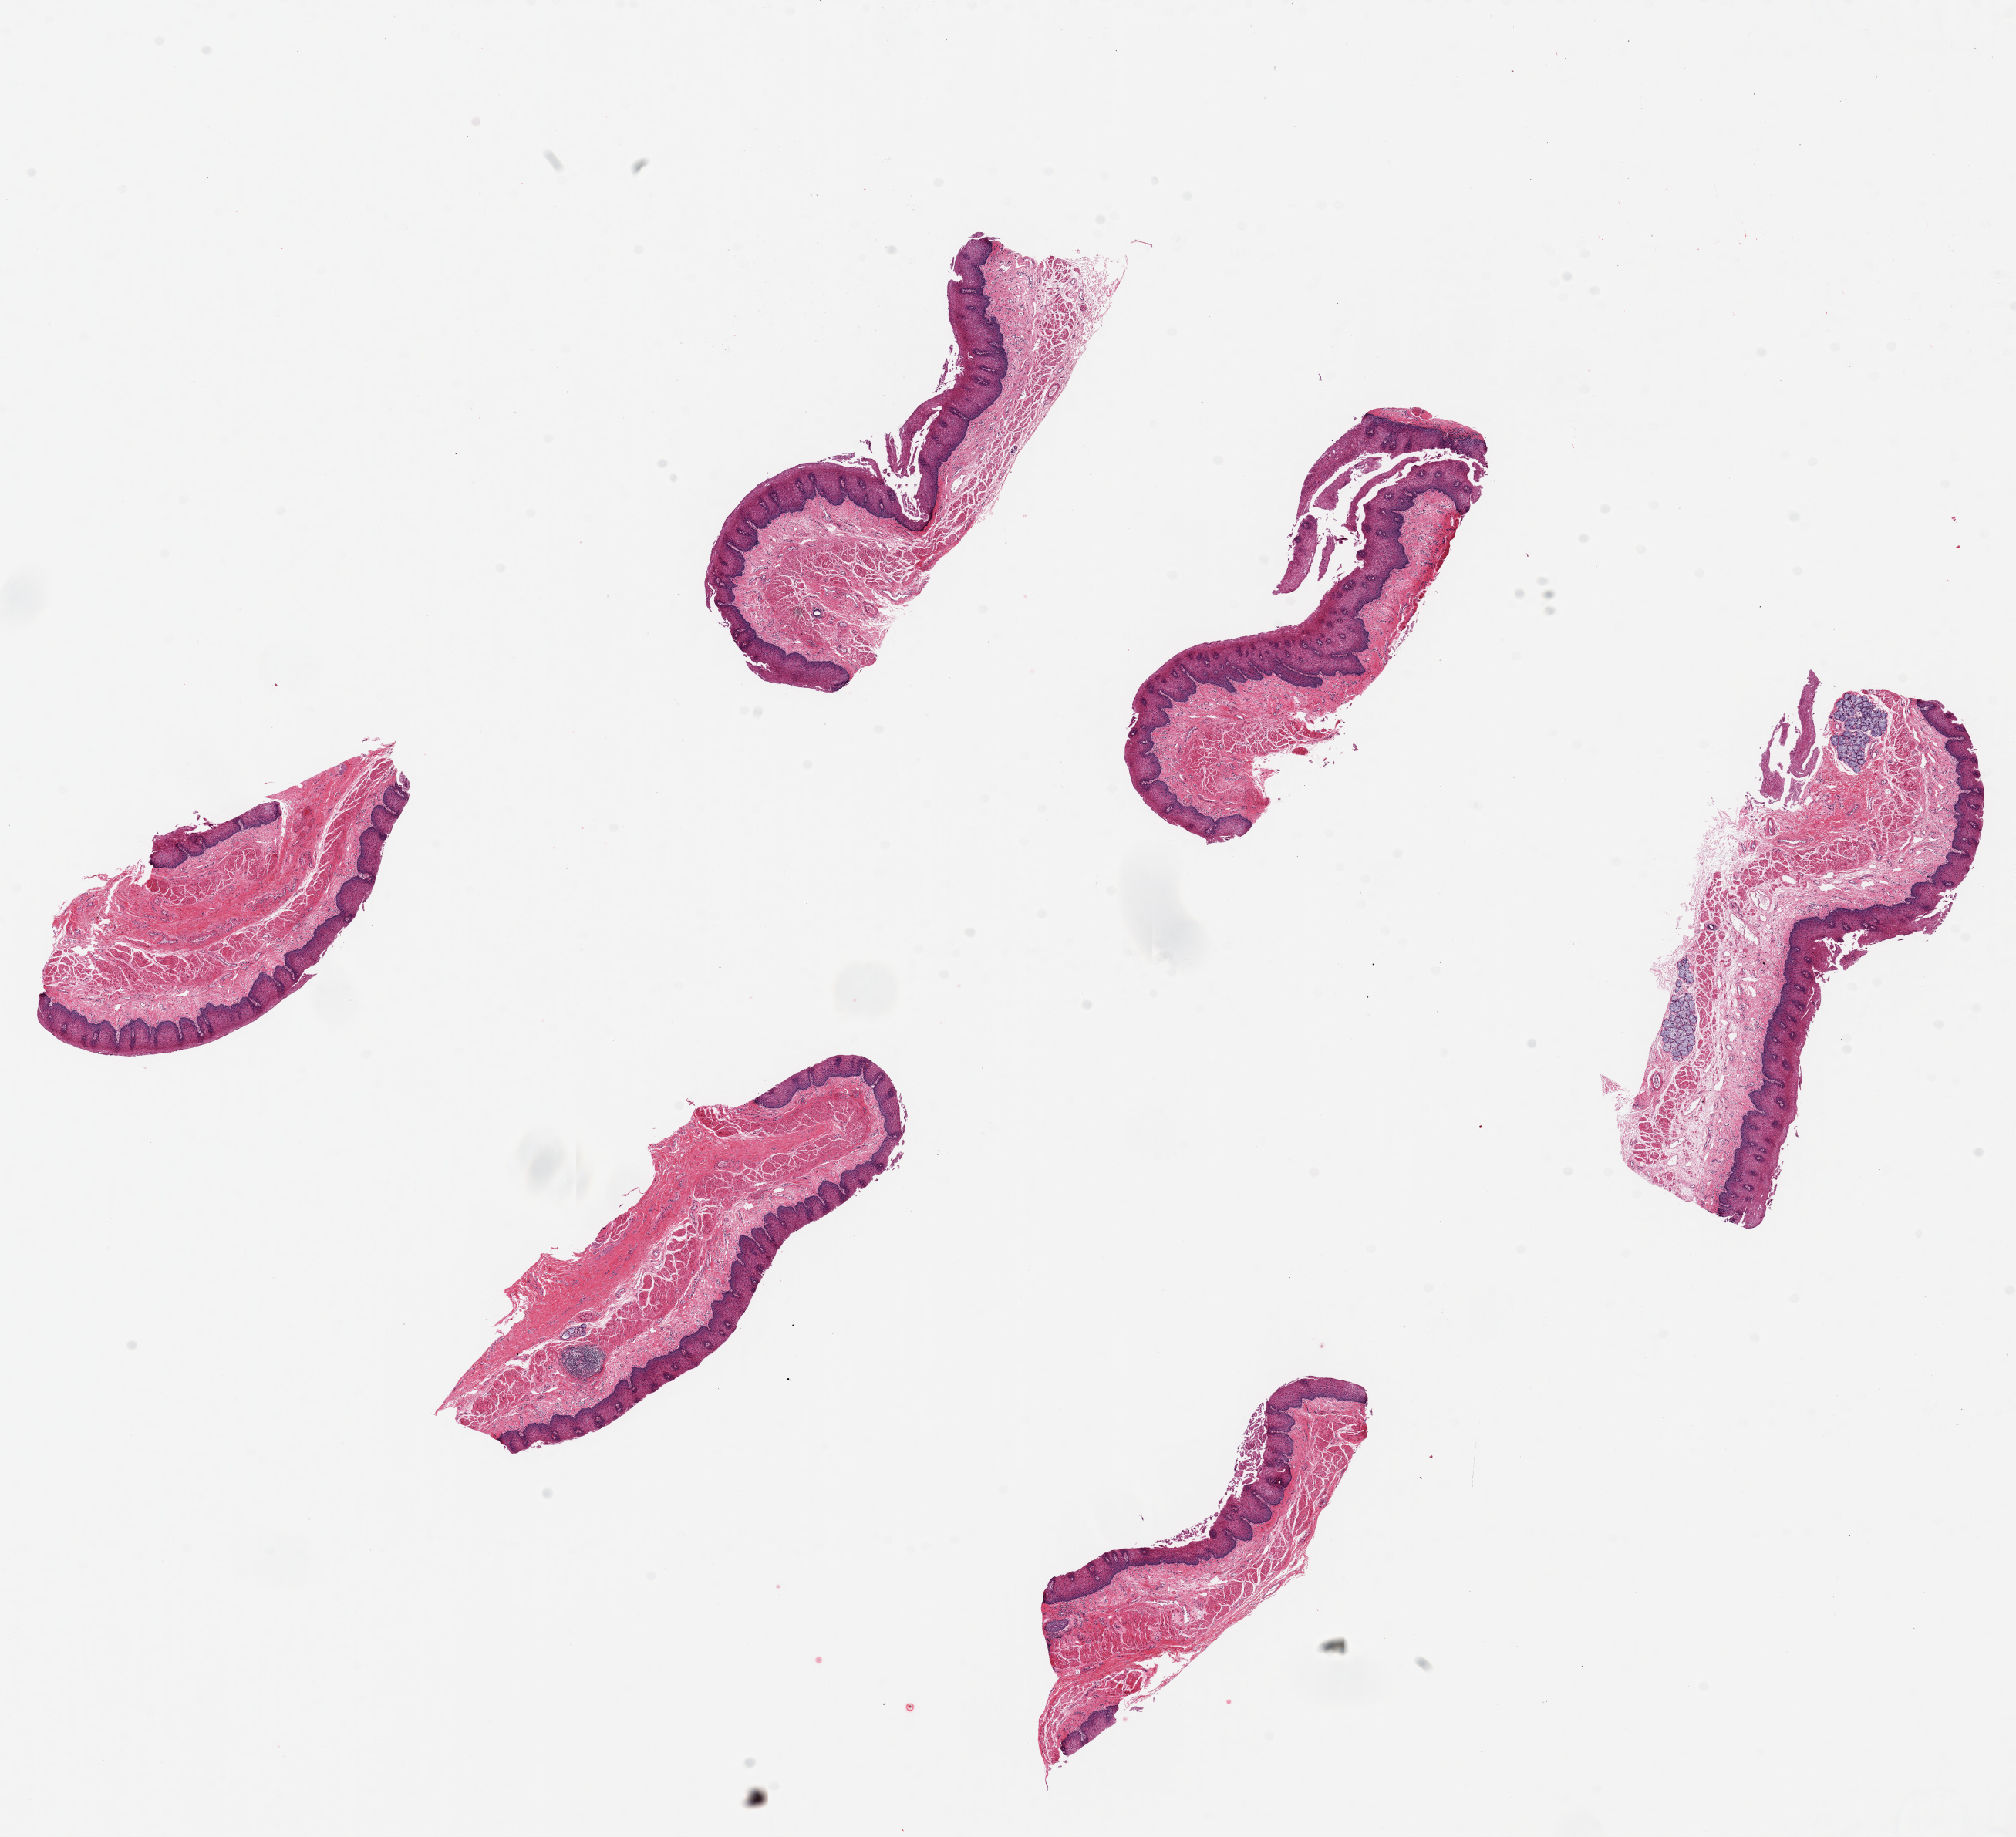
Hematoxylin and eosin (H&E) whole-slide image — shown as a low-resolution overview of the whole scanned area (about 20.7 x 18.8 mm, acquisition: 20x scan), PAXgene-fixed paraffin-embedded (PFPE) section, sampled site (target tissue): esophageal mucous membrane, donor tissue sample. Donor sex: male.
* reviewer comment on this tissue sample: 6 pieces ~5x2mm, ~15-20 squamous mucosa